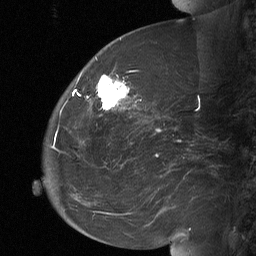
Breast MRI (dynamic contrast-enhanced), one sagittal slice; slice 24 of 64 in the series (ordered by position); dynamic contrast-enhanced study with each time point stored as its own series, time point 2 of 3 at this slice position (early post-contrast, ordered by acquisition time); 1.5 T; TE 4.8 ms, TR 27 ms; 2 mm slice thickness; 256 × 256 image matrix. Female patient, age 60 years. Case-level facts recorded for this patient, not image findings: setting: breast cancer imaged before/during neoadjuvant chemotherapy; receptor status: HR-positive, HER2-negative.
Outlined on this slice (semi-automatically segmented with operator editing):
- analysis volume of interest (the breast-tissue region the enhancement analysis was run in; not a lesion): bounding box <92,70,134,112> (left, top, right, bottom; pixels)
- tumour enhancement mask (voxels above the 90 % enhancement threshold inside the analysis volume of interest): <96,74,129,110>